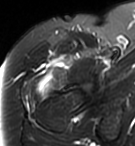
MRI of an extremity soft-tissue mass, one axial slice; position 84 of 95 along the scan axis; T2-weighted fat-saturated; MR volume resampled by the dataset authors to the PET/CT grid (not the native acquisition matrix); 3.27 mm slice thickness; 135 × 146 image matrix, field of view 132 × 143 mm. Female patient. From the clinical record (not read from this slice): histological type: pleiomorphic undifferentiated sarcoma; grade: high; site of the primary tumour: right quadricep.
Annotated regions visible in this slice (expert contour drawn on MRI and transferred to this co-registered scan by the dataset authors):
- gross tumour volume including surrounding oedema: bounding box (x1, y1, x2, y2) in pixels: (35, 68, 58, 101)